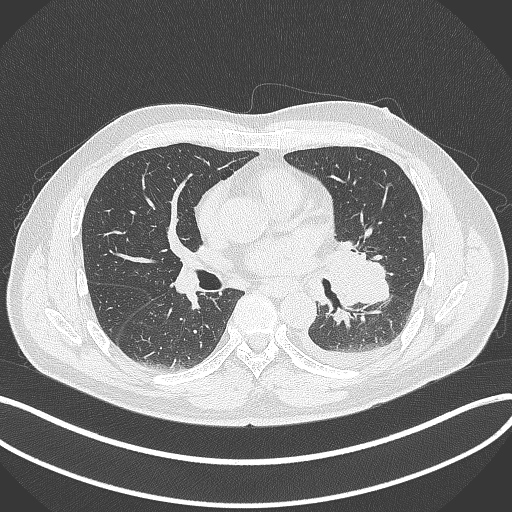
Chest CT, one axial slice. Slice 187 of 342 in the series (ordered by position). Reconstruction kernel B70f. Lung window (W 1500 / L -600 HU). 512 × 512 image matrix, field of view 400 × 400 mm. Male patient, age 58 years. From the clinical record (not read from this slice): clinical TNM (as recorded): T3 N1 M1b.
Outlined on this slice (bounding box drawn by a radiologist):
- lung tumour (recorded histology: small cell carcinoma): box from (x=325, y=235) to (x=389, y=307) px